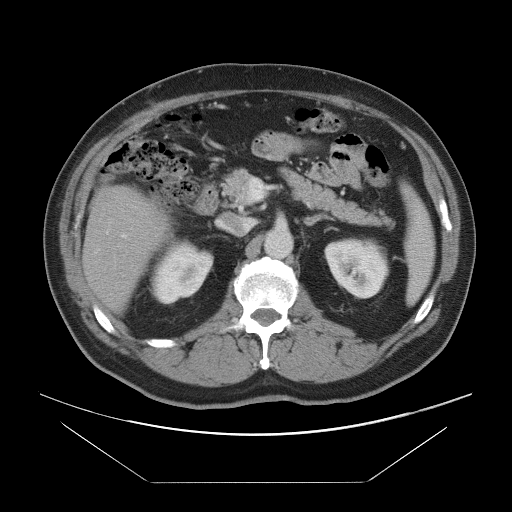
Contrast-enhanced abdominal CT, one axial slice. Position 45 of 97 along the scan axis. 120 kVp. Intravenous contrast given. Soft-tissue window (W 400 / L 40 HU). 512 × 512 image matrix, field of view 442 × 442 mm. Male patient, age 62 years. Case-level facts recorded for this patient, not image findings: diagnosis: colorectal cancer liver metastases, imaged before liver resection; multiple liver metastases: no; largest metastasis: 7 cm; disease in both lobes: yes.
Structures marked on this image (expert manual segmentation):
- hepatic veins: bounding box <106,231,109,234> (left, top, right, bottom; pixels)
- liver: <84,186,167,310>
- planned liver remnant (the part of the liver to remain after resection): <84,185,168,310>
- portal vein (with intrahepatic branches): <122,234,126,238>